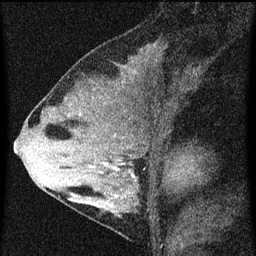
Breast MRI (dynamic contrast-enhanced), one sagittal slice. Slice 32 of 60 in the series (ordered by position). Dynamic contrast-enhanced series, image 2 of 3 at this slice position (ordered by acquisition). 1.5 T. TE 4.2 ms, TR 8 ms. 256 × 256 image matrix, field of view 180 × 180 mm. Patient: female, 33 years.
Annotated regions visible in this slice (semi-automatic segmentation, software-assisted and operator-edited):
- analysis volume of interest (the breast-tissue region the enhancement analysis was run in; not a lesion): bounding box [x1, y1, x2, y2] px = [67, 118, 161, 215]
- tumour enhancement mask (voxels above the 70 % enhancement threshold inside the analysis volume of interest): [103, 160, 135, 197]